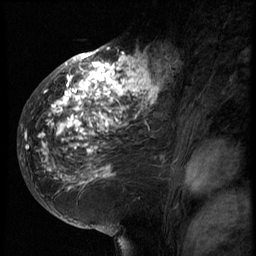
Breast MRI (dynamic contrast-enhanced), one sagittal slice. Position 37 of 66 along the scan axis. 3 images stored at this slice position (order not interpretable as contrast timing). 1.5 T. TE 4.2 ms, TR 8.9 ms. 2.5 mm slice thickness. 256 × 256 image matrix, field of view 200 × 200 mm. Patient: female, 39 years. Case-level facts recorded for this patient, not image findings: setting: breast cancer imaged before/during neoadjuvant chemotherapy; receptor status: HER2-positive.
Structures marked on this image (semi-automatically segmented with operator editing):
- analysis volume of interest (the breast-tissue region the enhancement analysis was run in; not a lesion): bounding box <29,44,166,196> (left, top, right, bottom; pixels)
- tumour enhancement mask (voxels above the 140 % enhancement threshold inside the analysis volume of interest): <39,47,166,183>